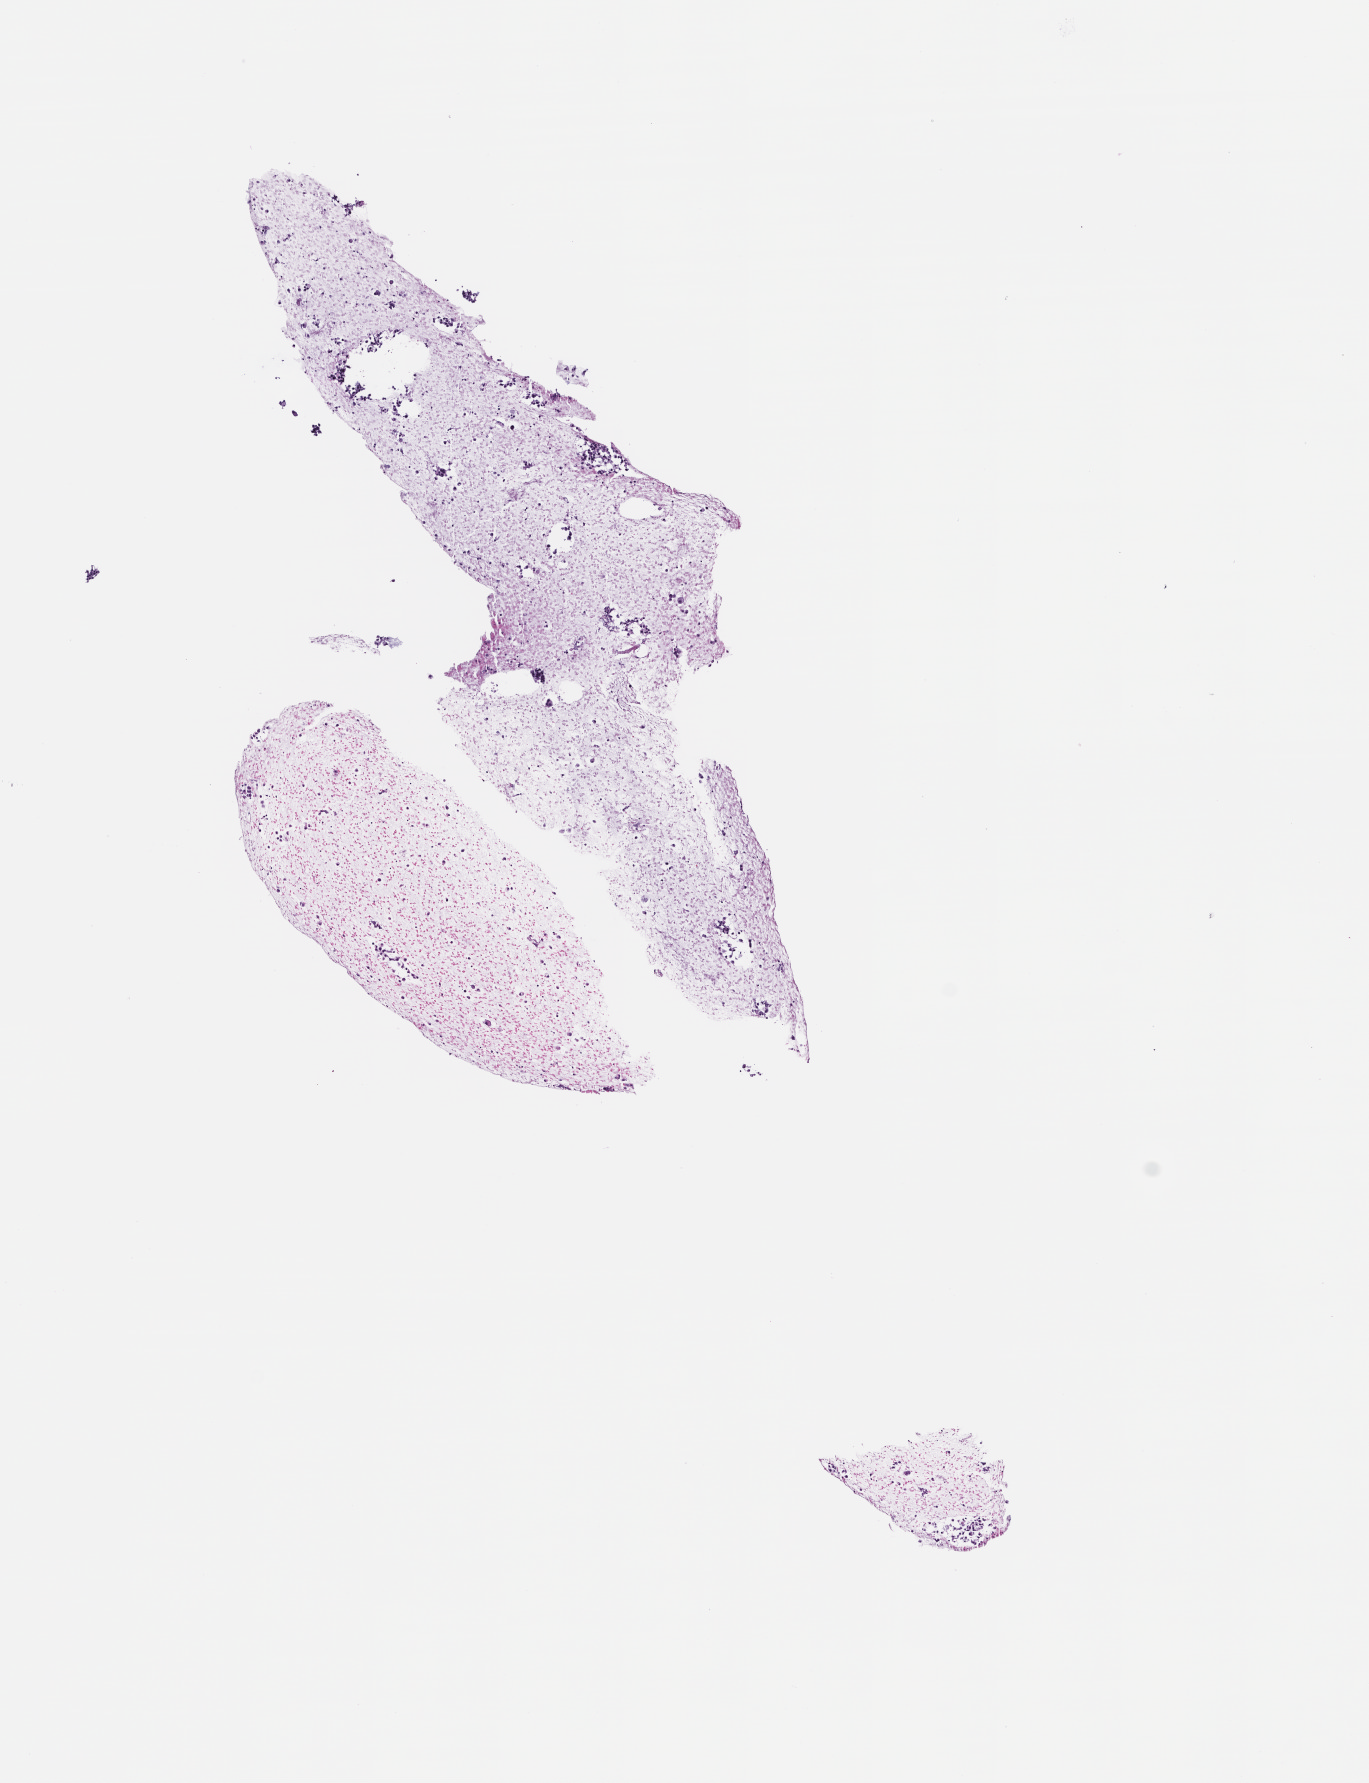
Haematoxylin and eosin whole-slide image — low-resolution overview of the scanned area, about 5.5 x 7.2 mm; formalin-fixed paraffin-embedded section; site: lung; archival tissue. Patient sex: female.
This section: primary tumor. Diagnosis: Non-Small Cell Lung Carcinoma.